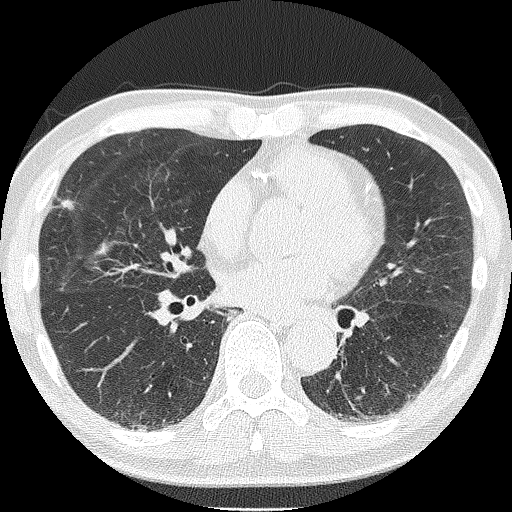
Low-dose screening chest CT, one axial slice. Reconstruction kernel FC51. 120 kVp. Lung window (W 1500 / L -600 HU). 512 × 512 image matrix, field of view 287 × 287 mm.
Outlined on this slice (manually delineated by an expert):
- lesion 1 (tumor, upper lobe of right lung): bounding box <58,199,78,210> (left, top, right, bottom; pixels)